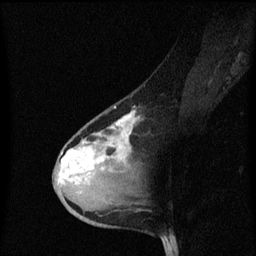
Breast MRI (dynamic contrast-enhanced), one sagittal slice. Slice 37 of 60 in the series (ordered by position). Dynamic contrast-enhanced series, image 2 of 3 at this slice position (ordered by acquisition). 1.5 T. TE 4.2 ms, TR 8.4 ms. 2 mm slice thickness. 256 × 256 image matrix. Female patient, age 38 years. Case-level facts recorded for this patient, not image findings: setting: breast cancer imaged before/during neoadjuvant chemotherapy; receptor status: HR-positive, HER2-negative.
Annotated regions visible in this slice (semi-automatically segmented with operator editing):
- analysis volume of interest (the breast-tissue region the enhancement analysis was run in; not a lesion): bounding box [x1, y1, x2, y2] px = [54, 102, 143, 205]
- tumour enhancement mask (voxels above the 70 % enhancement threshold inside the analysis volume of interest): [60, 112, 135, 183]